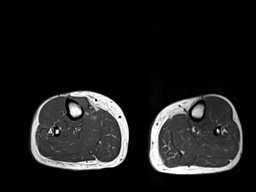
MRI of an extremity soft-tissue mass, one axial slice. Slice 13 of 32 in the series (ordered by position). 256 × 192 image matrix, field of view 375 × 281 mm. Female patient. From the clinical record (not read from this slice): histological type: undifferentiated – high grade; grade: high; site of the primary tumour: right thigh.
Outlined on this slice (expert manual segmentation):
- gross tumour volume (mass): bounding box (x1, y1, x2, y2) in pixels: (74, 95, 92, 114)